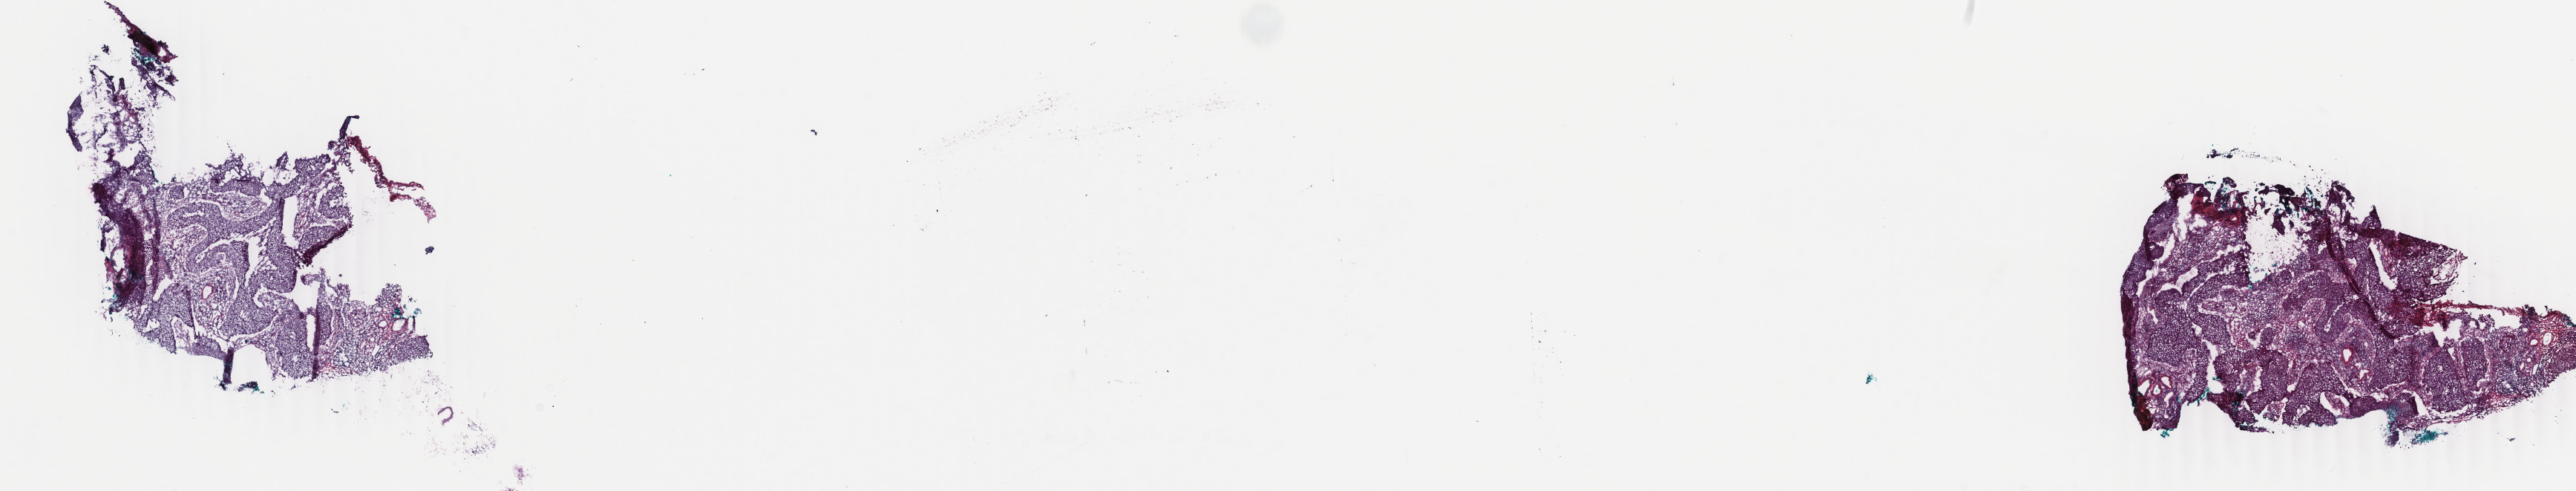
H&E-stained whole-slide image, whole scanned area (about 27.6 x 5.3 mm, acquisition: 40x scan) shown as a low-resolution overview. Frozen section from the top of the tissue portion. Sample: primary tumour, cervix. Patient: female, age at initial diagnosis 53 years. Histologic grade: G3 (poorly differentiated). Slide review estimates, as recorded: tumour cells 80%, tumour nuclei 80%, normal cells 0%, stromal cells 20%, necrosis 0%. Inflammatory infiltration, as recorded: lymphocyte infiltration 40%, monocyte infiltration 1%, neutrophil infiltration 2%.
- FIGO stage: IB
- lymph nodes positive (case pathology): 0 of 24 examined
- histologic diagnosis: Squamous cell carcinoma, NOS (cervix uteri)